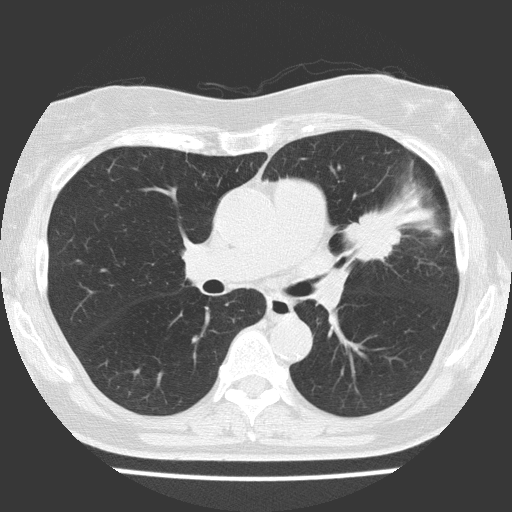
Low-dose screening chest CT, one axial slice; position 86 of 151 along the scan axis; reconstruction kernel FC51; 120 kVp; lung window (W 1500 / L -600 HU); 2 mm slice thickness; 512 × 512 image matrix, field of view 309 × 309 mm.
Outlined on this slice (outlined manually by an expert reader):
- lesion 1 (tumor, upper lobe of left lung): bounding box (x1, y1, x2, y2) in pixels: (345, 210, 402, 261)